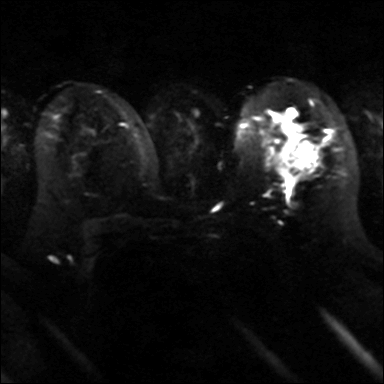
Breast MRI, one axial slice. Diffusion-weighted series; image 2 of 4 stored at this slice position (different b-values; order by instance number). 3 T. 4 mm slice thickness. 384 × 384 image matrix, field of view 320 × 320 mm. Female patient.
Structures marked on this image (expert manual segmentation):
- tumour on diffusion-weighted imaging: bounding box [x1, y1, x2, y2] px = [293, 141, 317, 168]